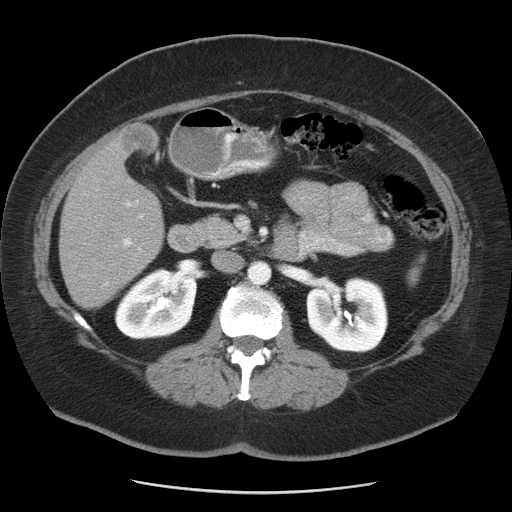
Contrast-enhanced abdominal CT, one axial slice; position 20 of 55 along the scan axis; reconstruction kernel STANDARD; 120 kVp; intravenous contrast given; soft-tissue window (W 400 / L 40 HU); 512 × 512 image matrix, field of view 380 × 380 mm. Female patient, age 52 years. From the clinical record (not read from this slice): diagnosis: colorectal cancer liver metastases, imaged before liver resection; multiple liver metastases: yes; largest metastasis: 2.5 cm; disease in both lobes: yes.
Annotated regions visible in this slice (manually delineated by an expert):
- liver: bounding box [x1, y1, x2, y2] px = [60, 123, 164, 308]
- planned liver remnant (the part of the liver to remain after resection): [60, 188, 163, 308]
- portal vein (with intrahepatic branches): [96, 187, 144, 285]
- liver metastasis: [119, 126, 157, 154]